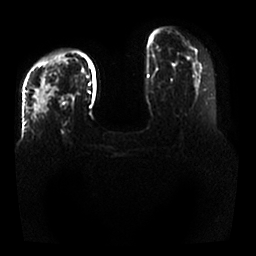
Breast MRI, one axial slice. Slice 13 of 25 in the series (ordered by position). Diffusion-weighted series; image 2 of 4 stored at this slice position (different b-values; order by instance number). 1.5 T. 4 mm slice thickness. 256 × 256 image matrix, field of view 350 × 350 mm. Female patient.
Structures marked on this image (expert manual segmentation):
- tumour on diffusion-weighted imaging: bounding box [x1, y1, x2, y2] px = [33, 56, 67, 116]